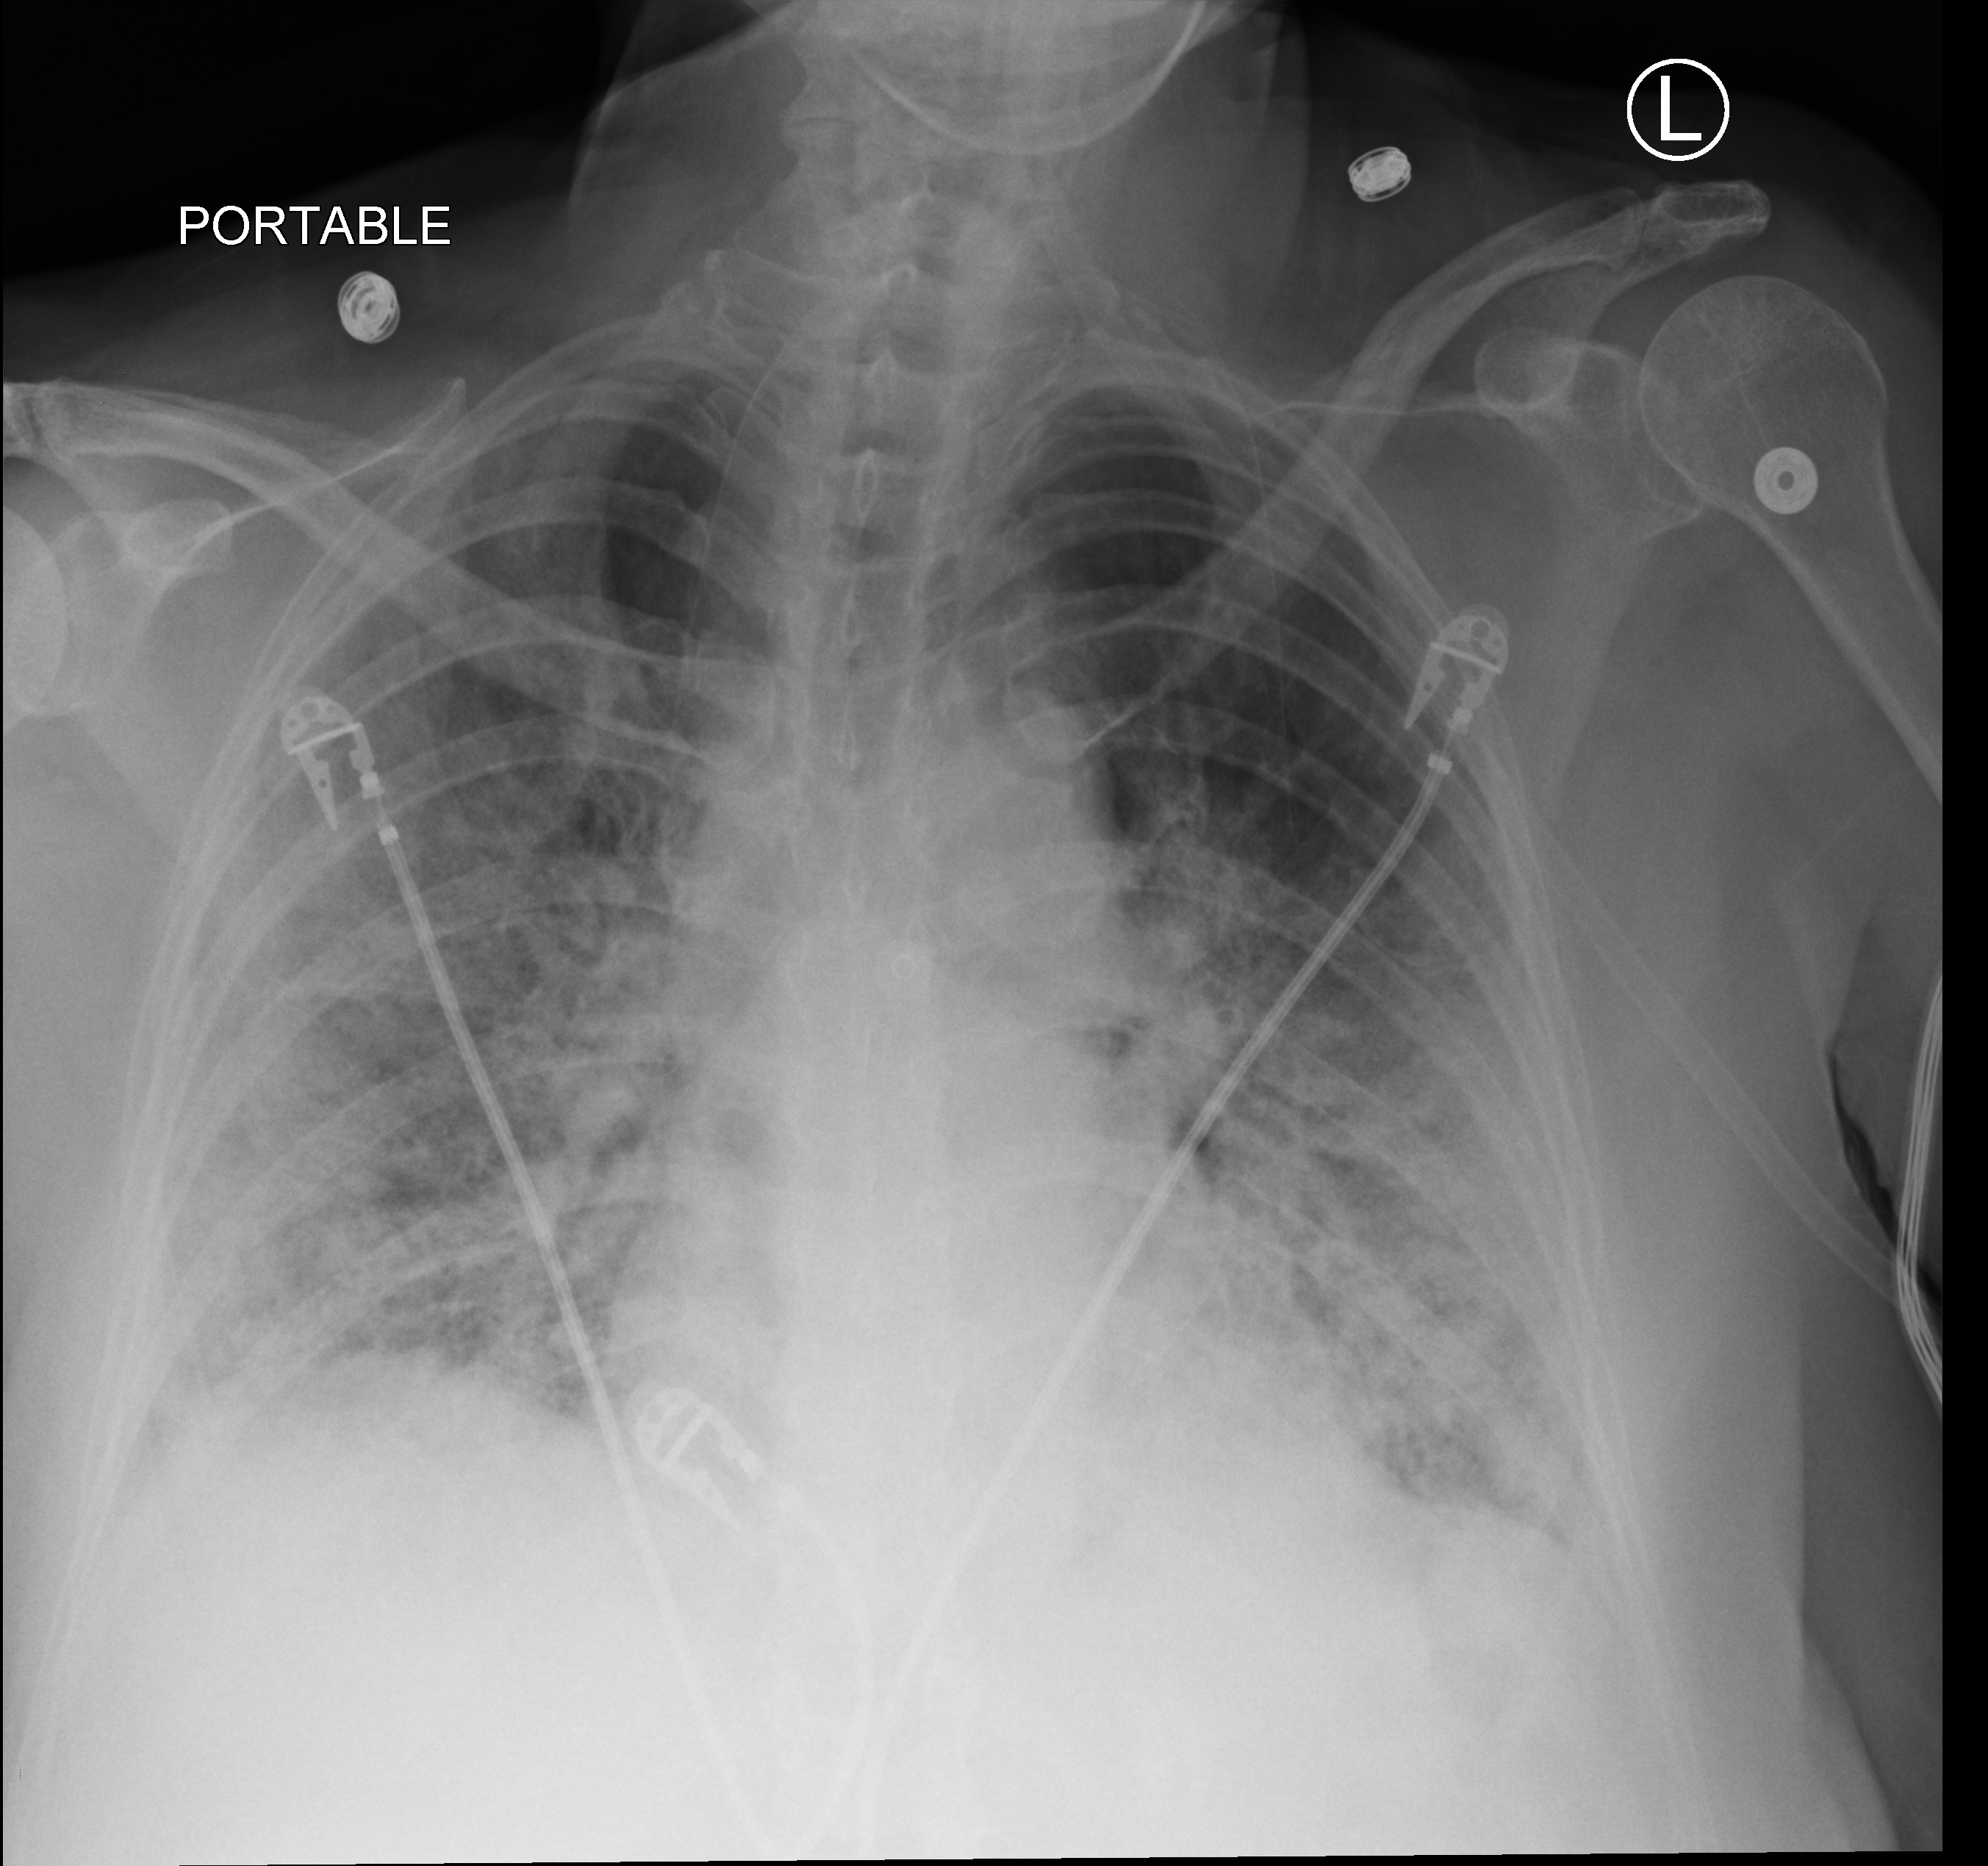
Portable chest radiograph. Patient hospitalised with COVID-19; female, aged 60–74 years.
Hospital-stay facts (about this admission, not read from this image; timing relative to this image not recorded):
- length of hospital stay: 43 days